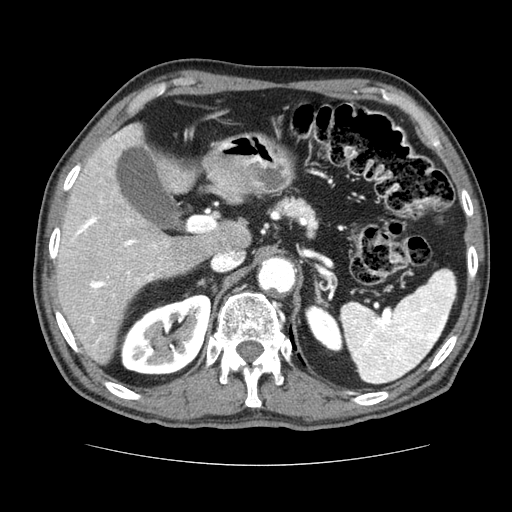
Contrast-enhanced abdominal CT (liver protocol), one axial slice; reconstruction kernel STANDARD; 120 kVp; soft-tissue window (W 400 / L 40 HU); 2.5 mm slice thickness; 512 × 512 image matrix. From the clinical record (not read from this slice): diagnosis: hepatocellular carcinoma (patient treated with transarterial chemoembolisation; whether this scan precedes or follows treatment is not stated here); TNM stage (as recorded): Stage-I; Child-Pugh class: A; tumour nodularity: uninodular.
Structures marked on this image (semi-automatic segmentation, software-assisted and operator-edited):
- liver parenchyma outside the tumour (the mass and vessels are separate outlines, so this box may not span the whole liver): bounding box [x1, y1, x2, y2] px = [56, 124, 232, 362]
- liver vessels: [71, 134, 157, 343]